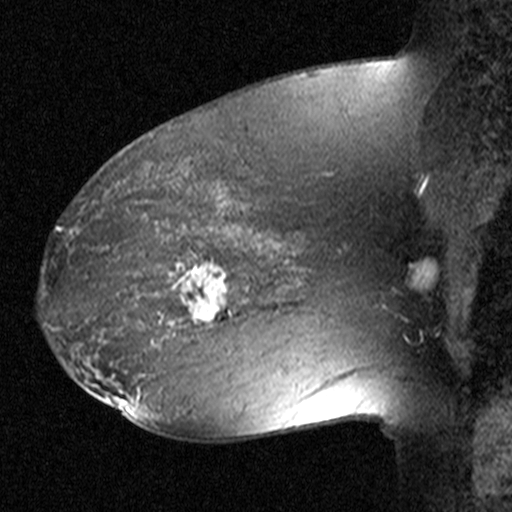
Breast MRI (dynamic contrast-enhanced), one sagittal slice; position 28 of 44 along the scan axis; dynamic contrast-enhanced study with each time point stored as its own series, time point 2 of 3 at this slice position (early post-contrast, ordered by acquisition time); 1.5 T; TE 4.5 ms, TR 11 ms; 512 × 512 image matrix, field of view 200 × 200 mm. Female patient, age 38 years. From the clinical record (not read from this slice): setting: breast cancer imaged before/during neoadjuvant chemotherapy; receptor status: HR-positive, HER2-negative.
Structures marked on this image (semi-automatic segmentation, software-assisted and operator-edited):
- analysis volume of interest (the breast-tissue region the enhancement analysis was run in; not a lesion): bounding box [x1, y1, x2, y2] px = [152, 236, 253, 335]
- tumour enhancement mask (voxels above the 90 % enhancement threshold inside the analysis volume of interest): [169, 258, 231, 327]